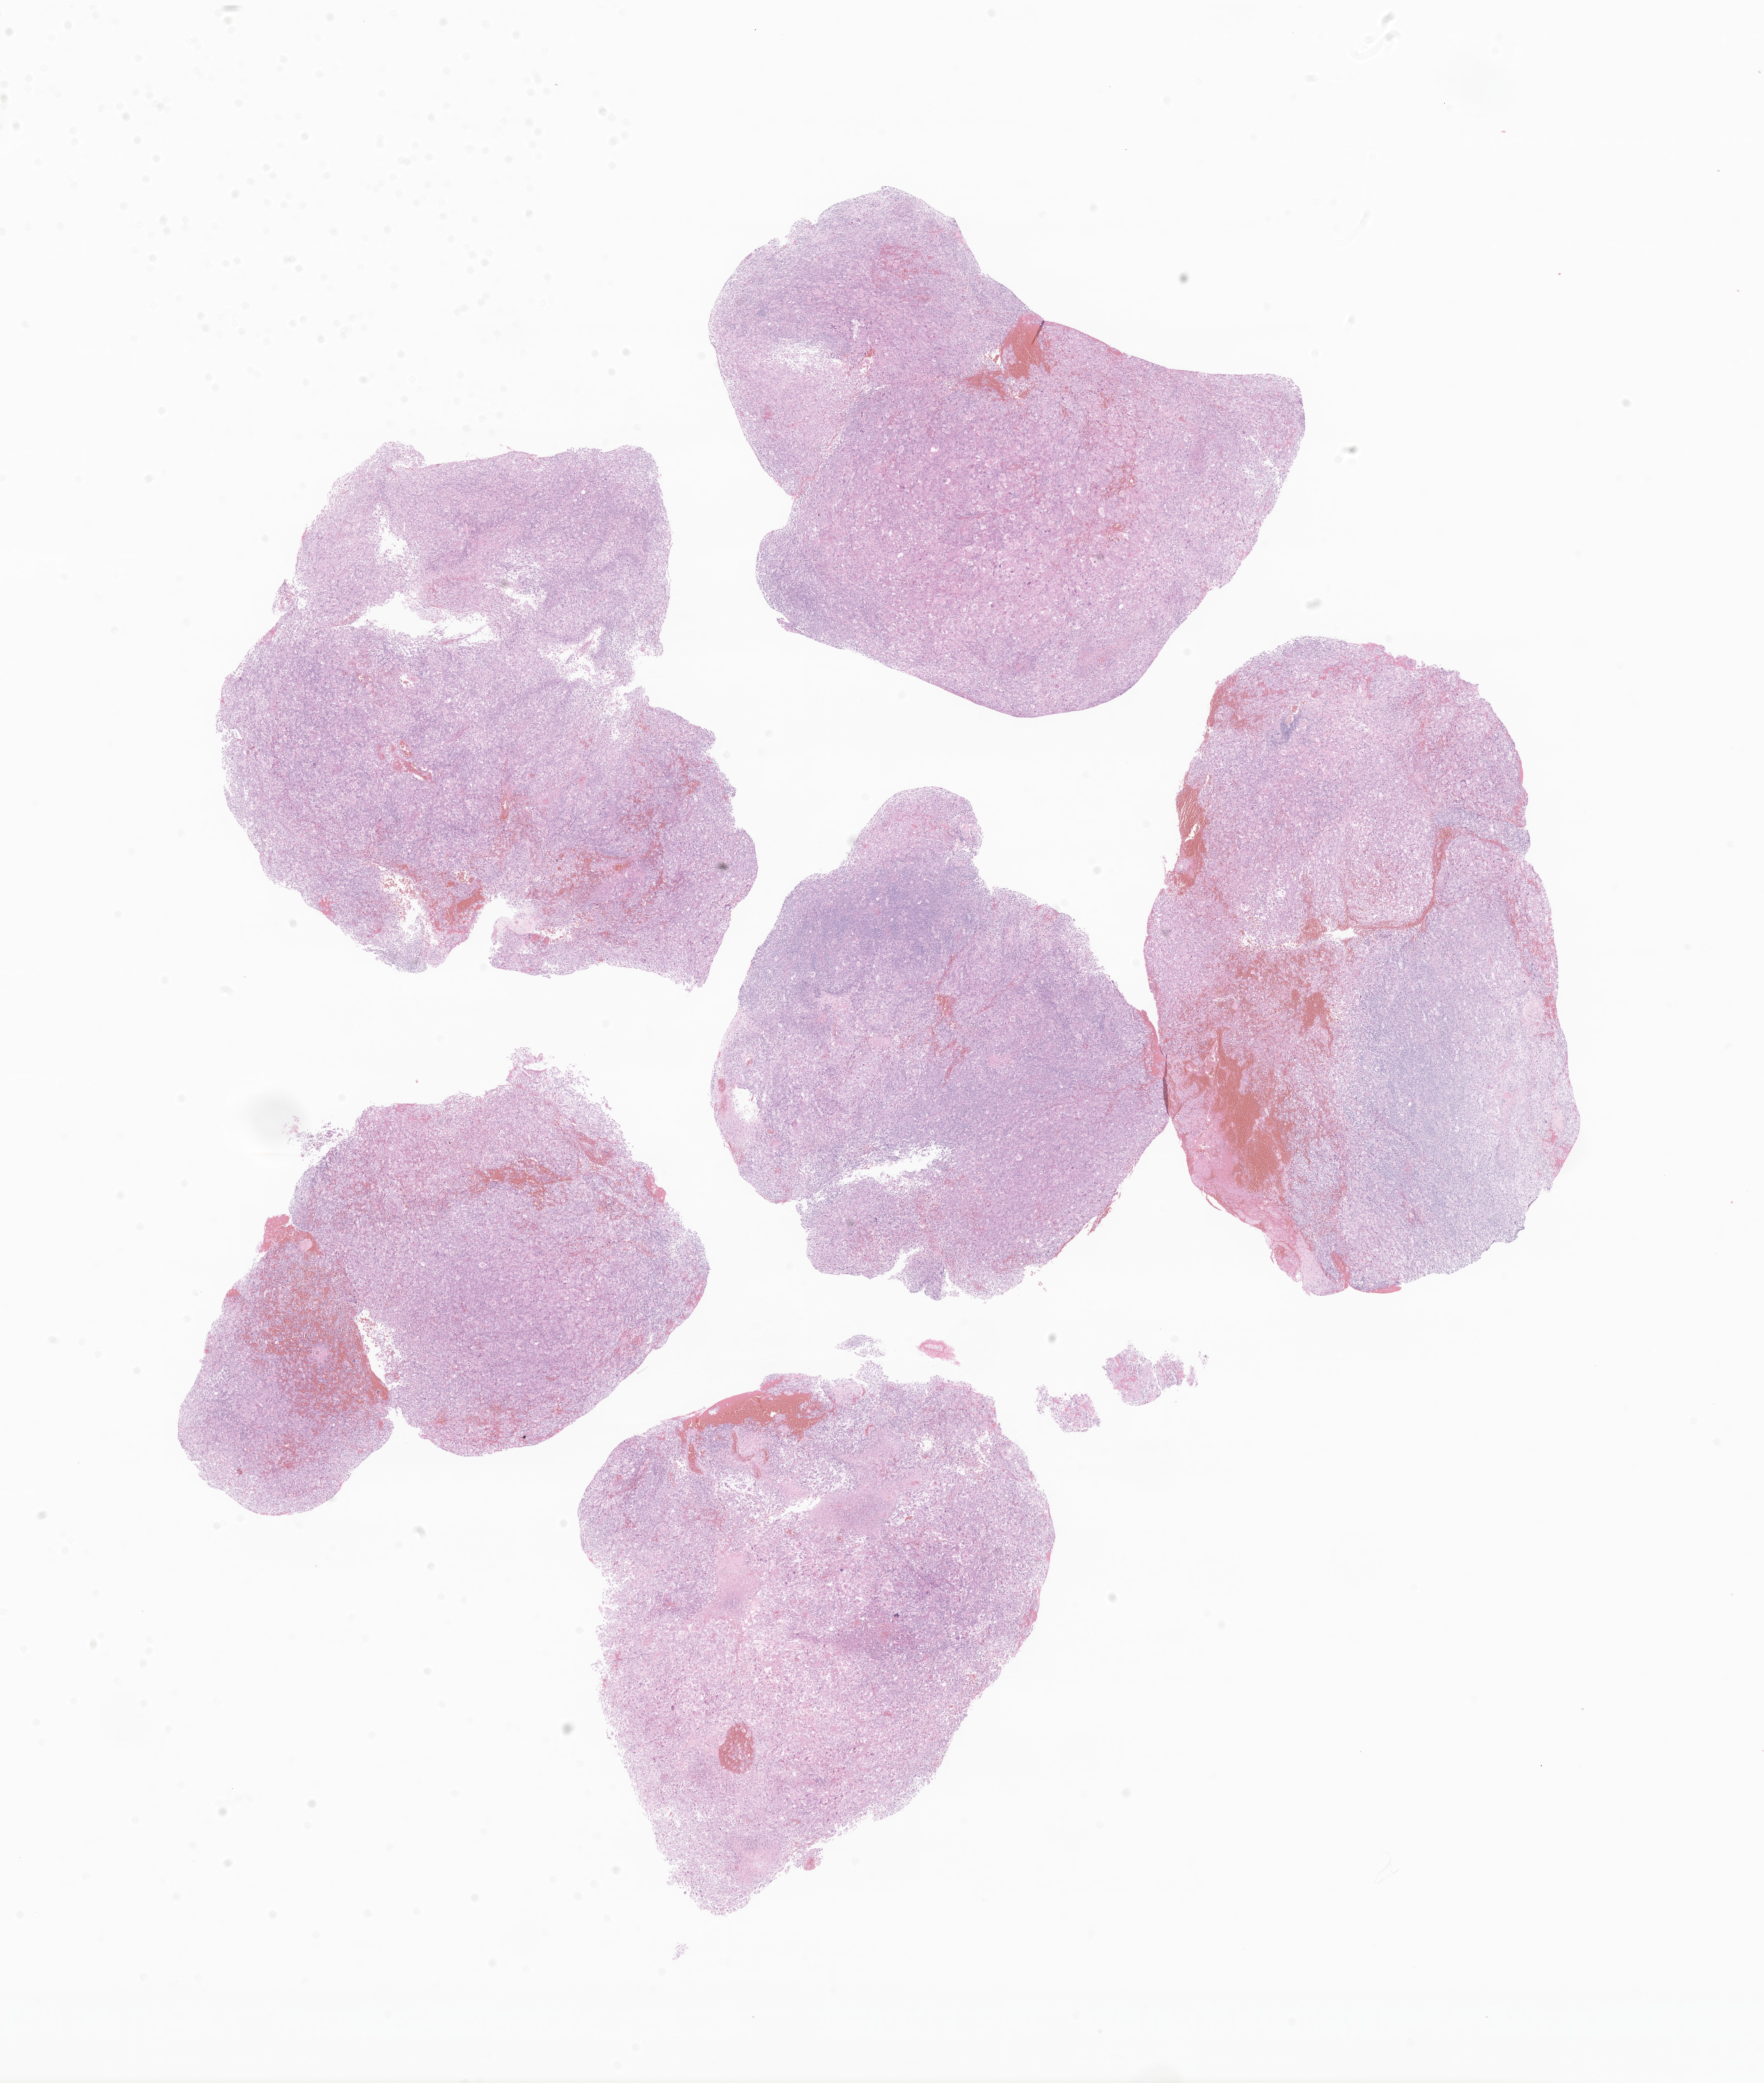
Whole-slide image, hematoxylin and eosin (H&E) stain of tumor tissue from the brain — a low-resolution overview of the entire scanned area, about 18.1 x 21.4 mm; formalin-fixed, paraffin-embedded (FFPE) tissue. Male patient, age 76 months.
- recorded diagnosis: Glioma, malignant